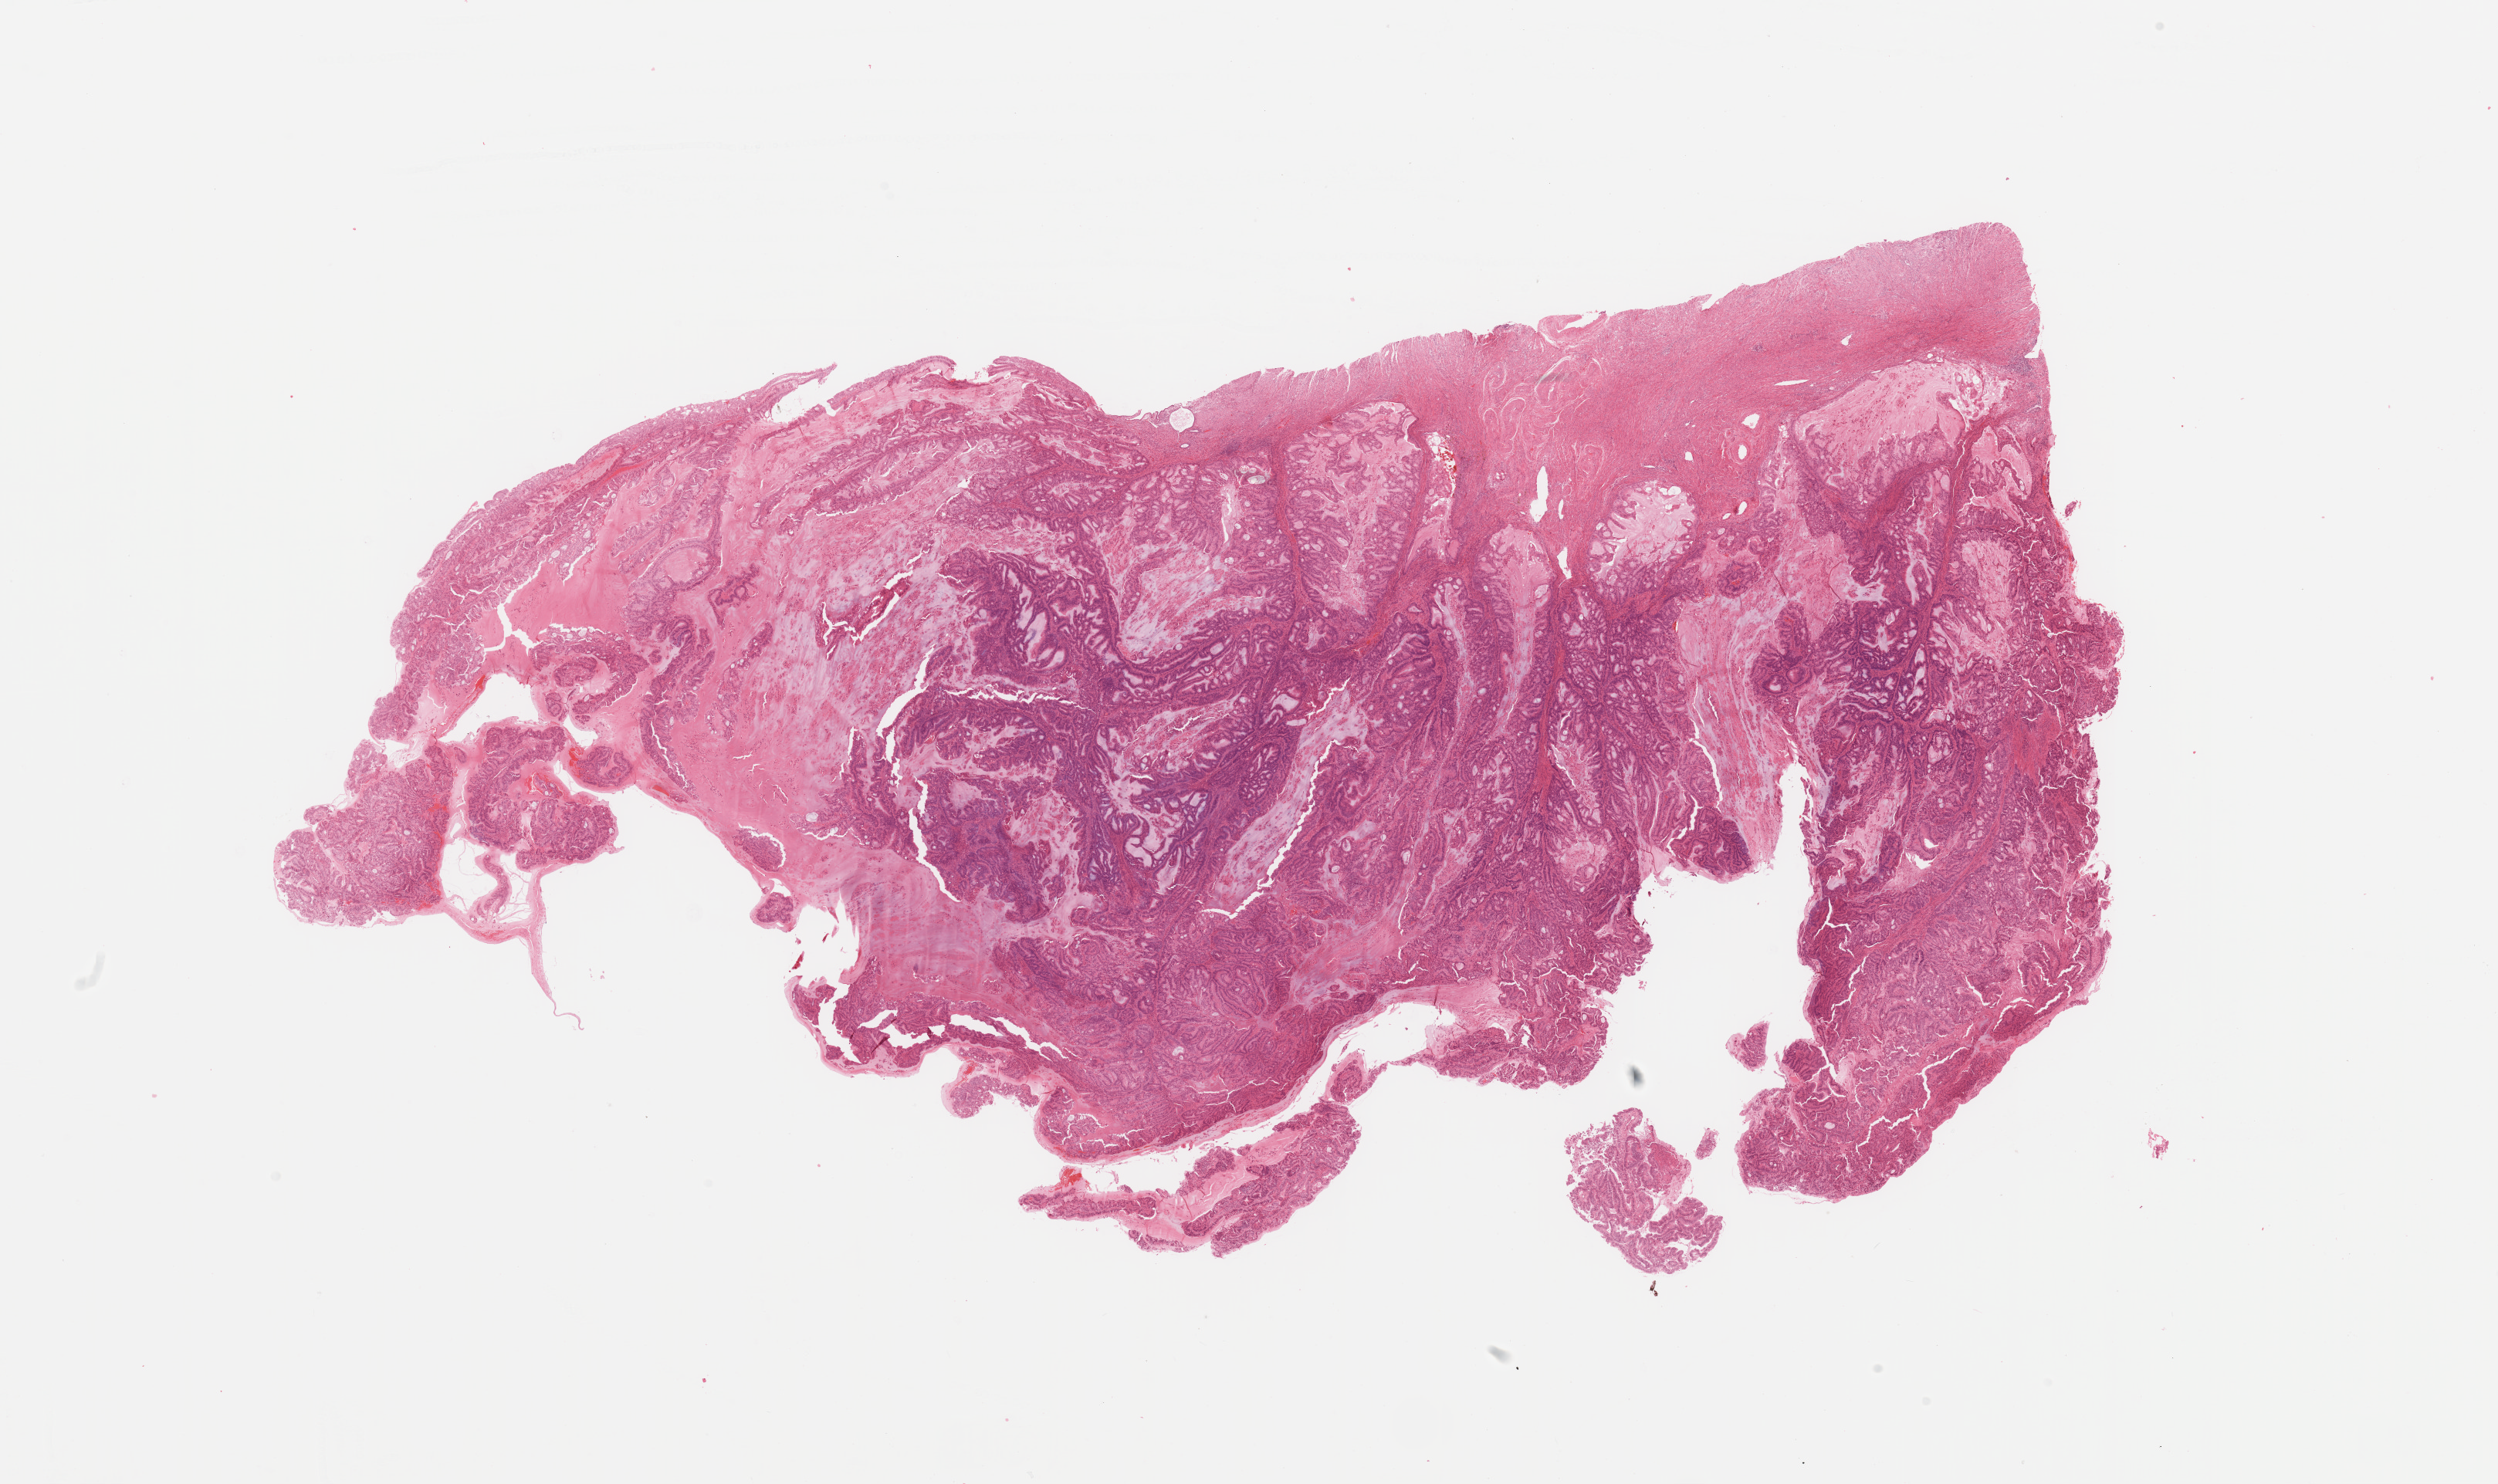
Digitized Hematoxylin and eosin (H&E) stained tissue section (whole slide) — a low-resolution overview of the entire scanned area, about 25.6 x 15.2 mm (from a 20x scan); tumour tissue sample, uterus. Patient: female, age 77 years. Histologic grade: G1 (well differentiated).
• diagnosis: Endometrioid adenocarcinoma, NOS